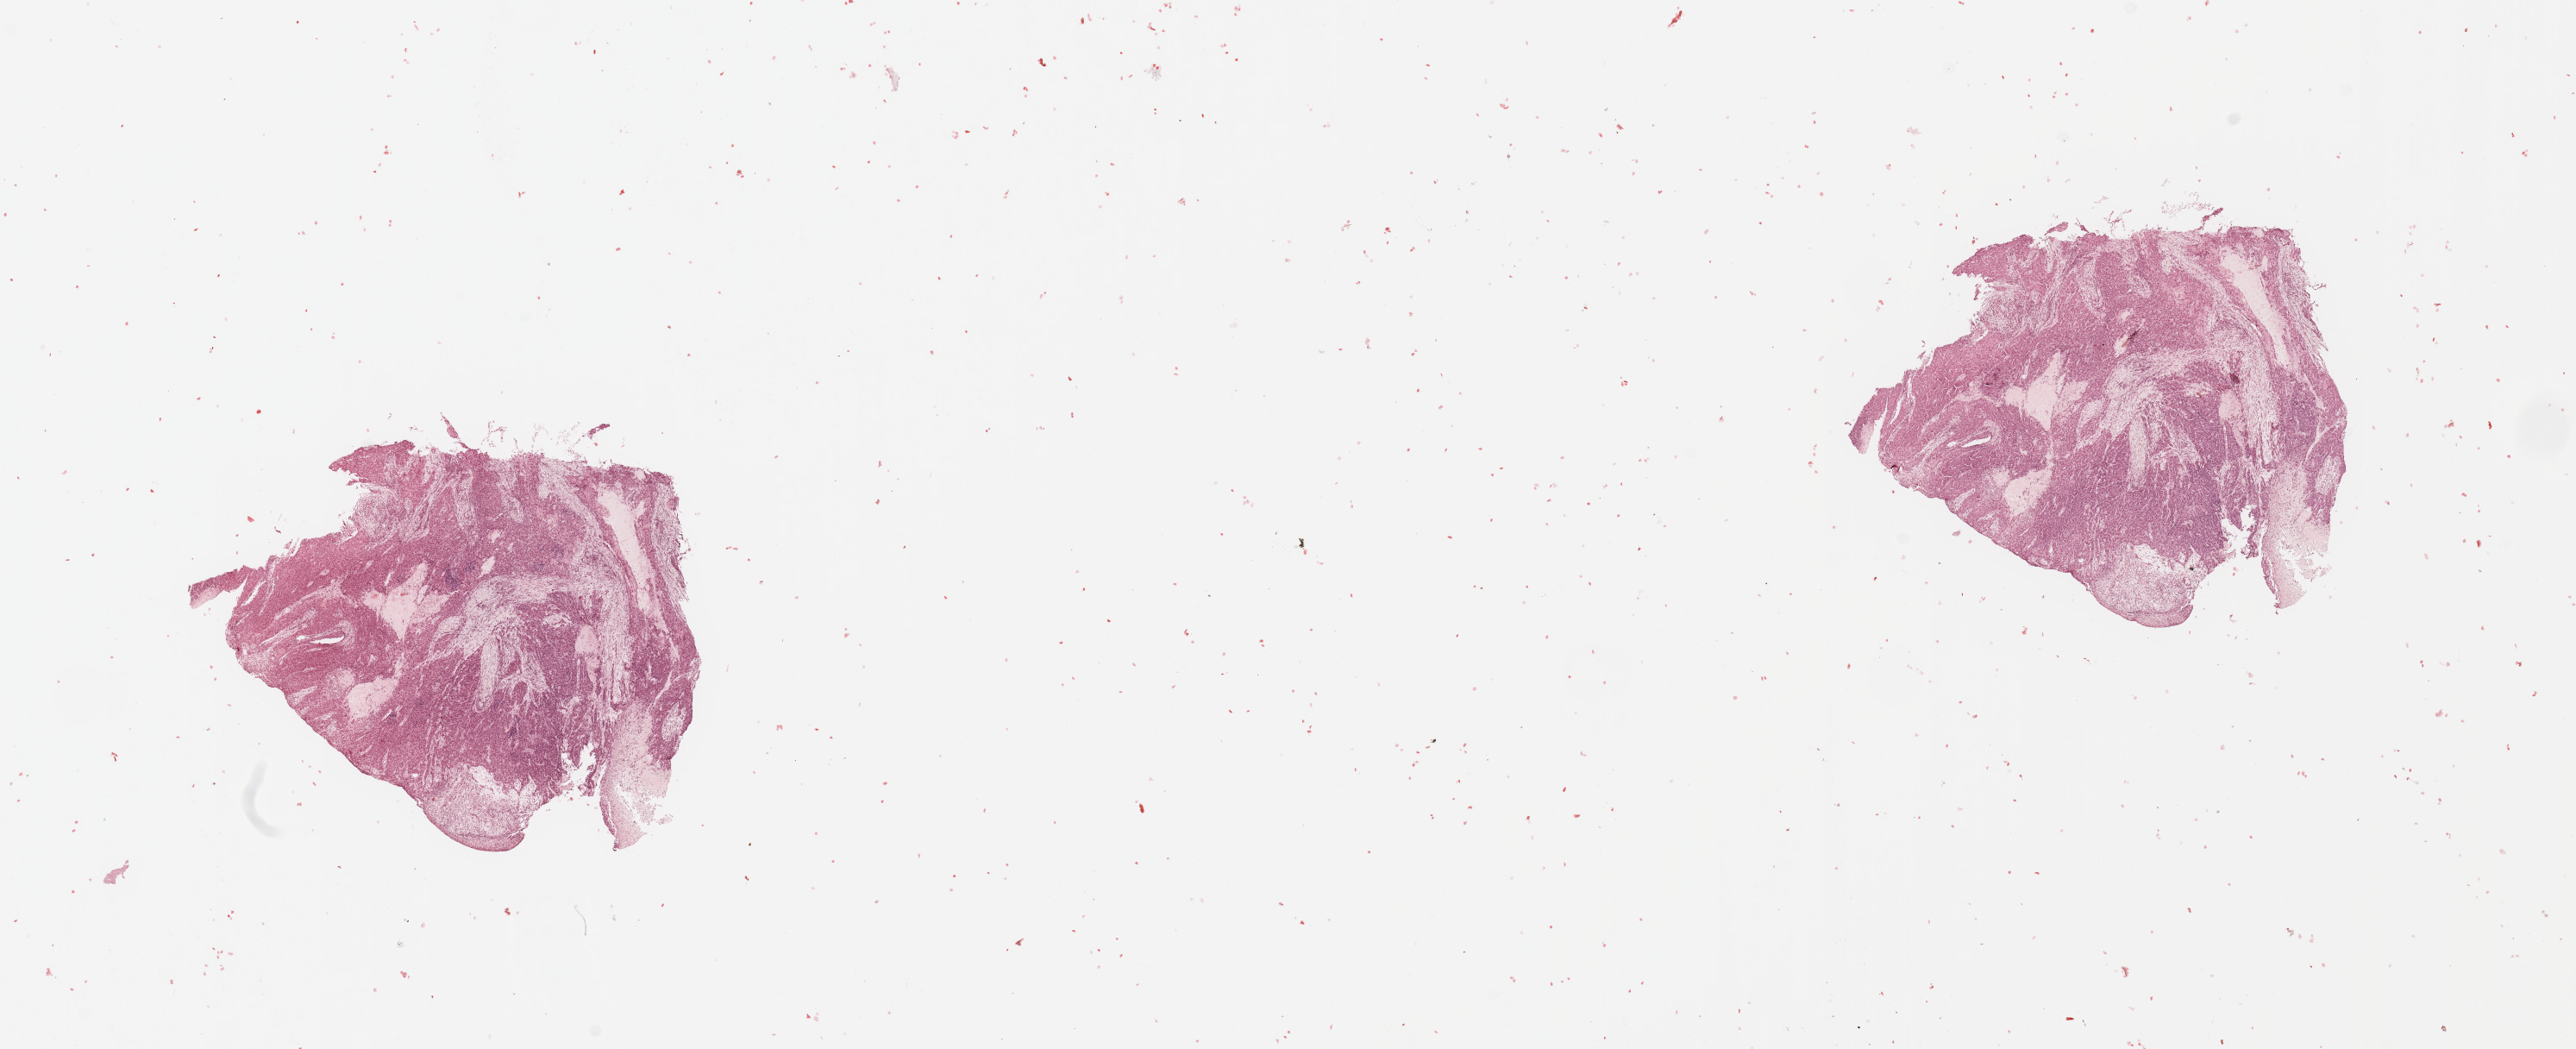
Whole-slide histology image, H&E-stained, low-resolution overview of the scanned area, about 23.6 x 9.6 mm (acquisition: 20x scan), head and neck, tissue type not recorded. 68-year-old male patient.
* patient diagnosis: Squamous cell carcinoma, NOS (larynx, NOS)